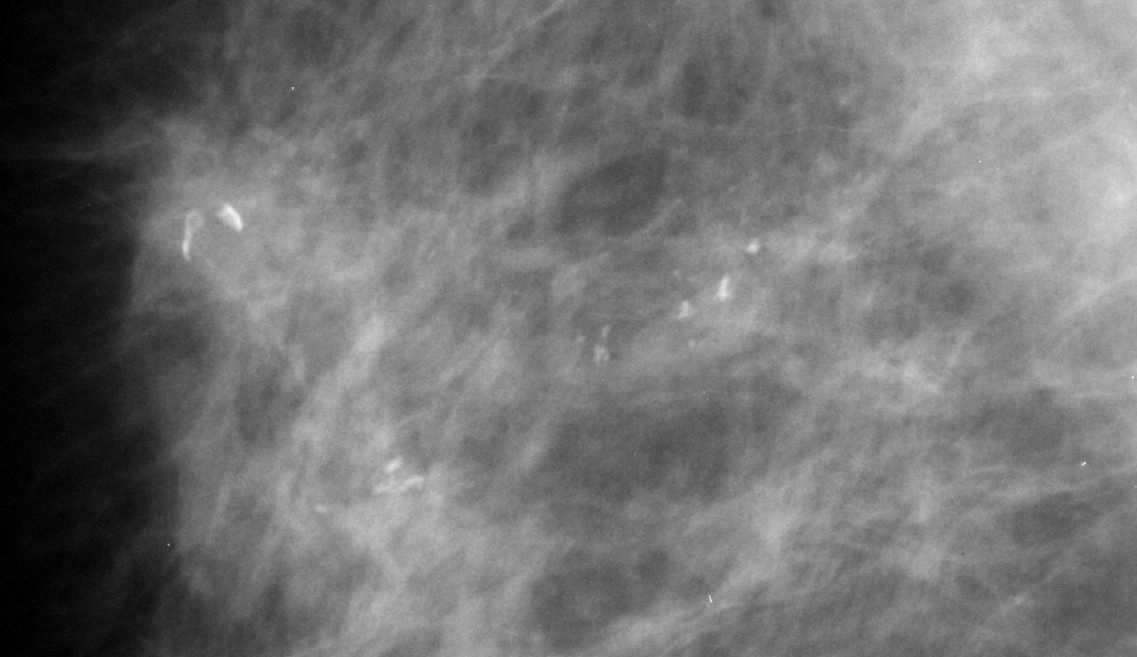
Crop from a digitized film mammogram around one marked abnormality; right breast; MLO view; BI-RADS breast density category 2 (scale 1–4).
Finding: calcifications, morphology pleomorphic, distribution segmental; BI-RADS assessment category 5; pathology (as recorded): malignant.